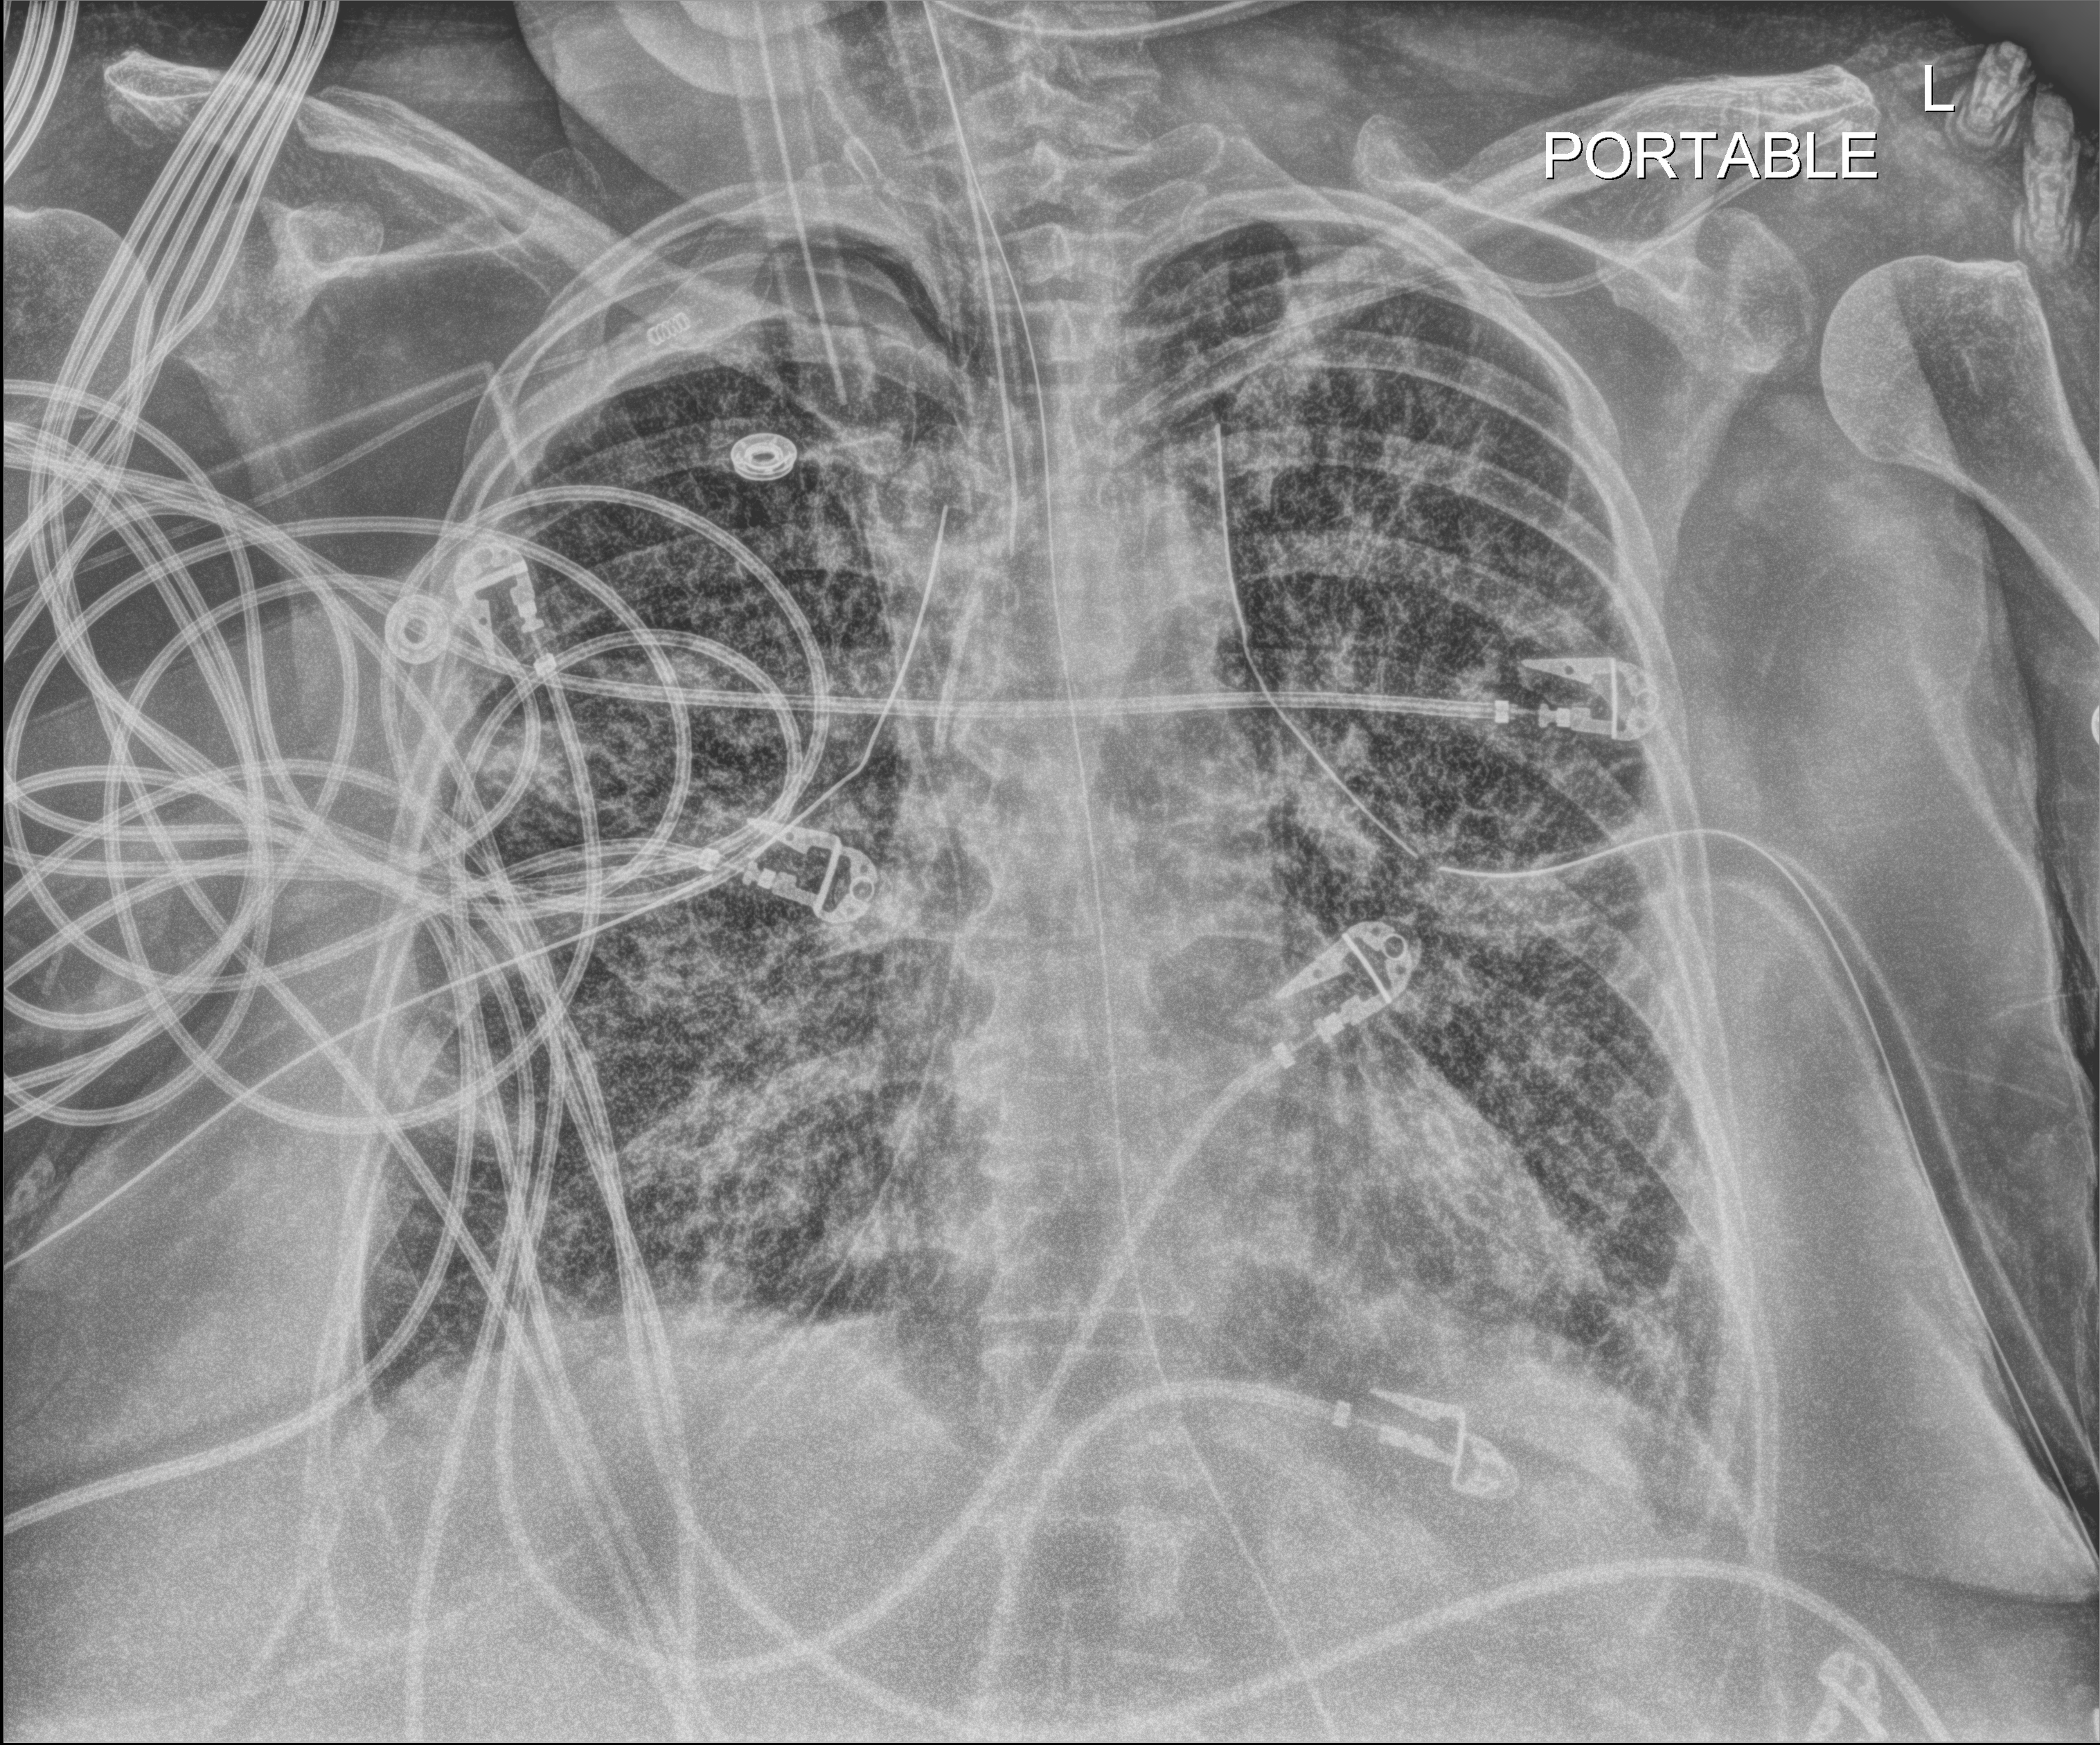
Bedside chest radiograph (digital radiography), anteroposterior (AP) projection. Patient hospitalised with COVID-19; female, aged 60–74 years.
Admission-level facts for this patient (not findings on this image; timing relative to this image not recorded):
- admitted to intensive care during this hospital stay: yes
- mechanically ventilated during this hospital stay: yes